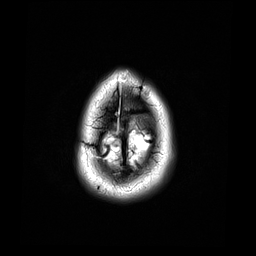
Brain MRI from a brain-tumour surgery series, one axial slice. Slice 4 of 44 in the series (ordered by position). 256 × 256 image matrix. Case-level facts recorded for this patient, not image findings: histopathology: Astrocytoma; WHO grade: 4.
Annotated regions visible in this slice (outlined manually by an expert reader):
- tumour: bounding box [x1, y1, x2, y2] px = [110, 143, 113, 148]